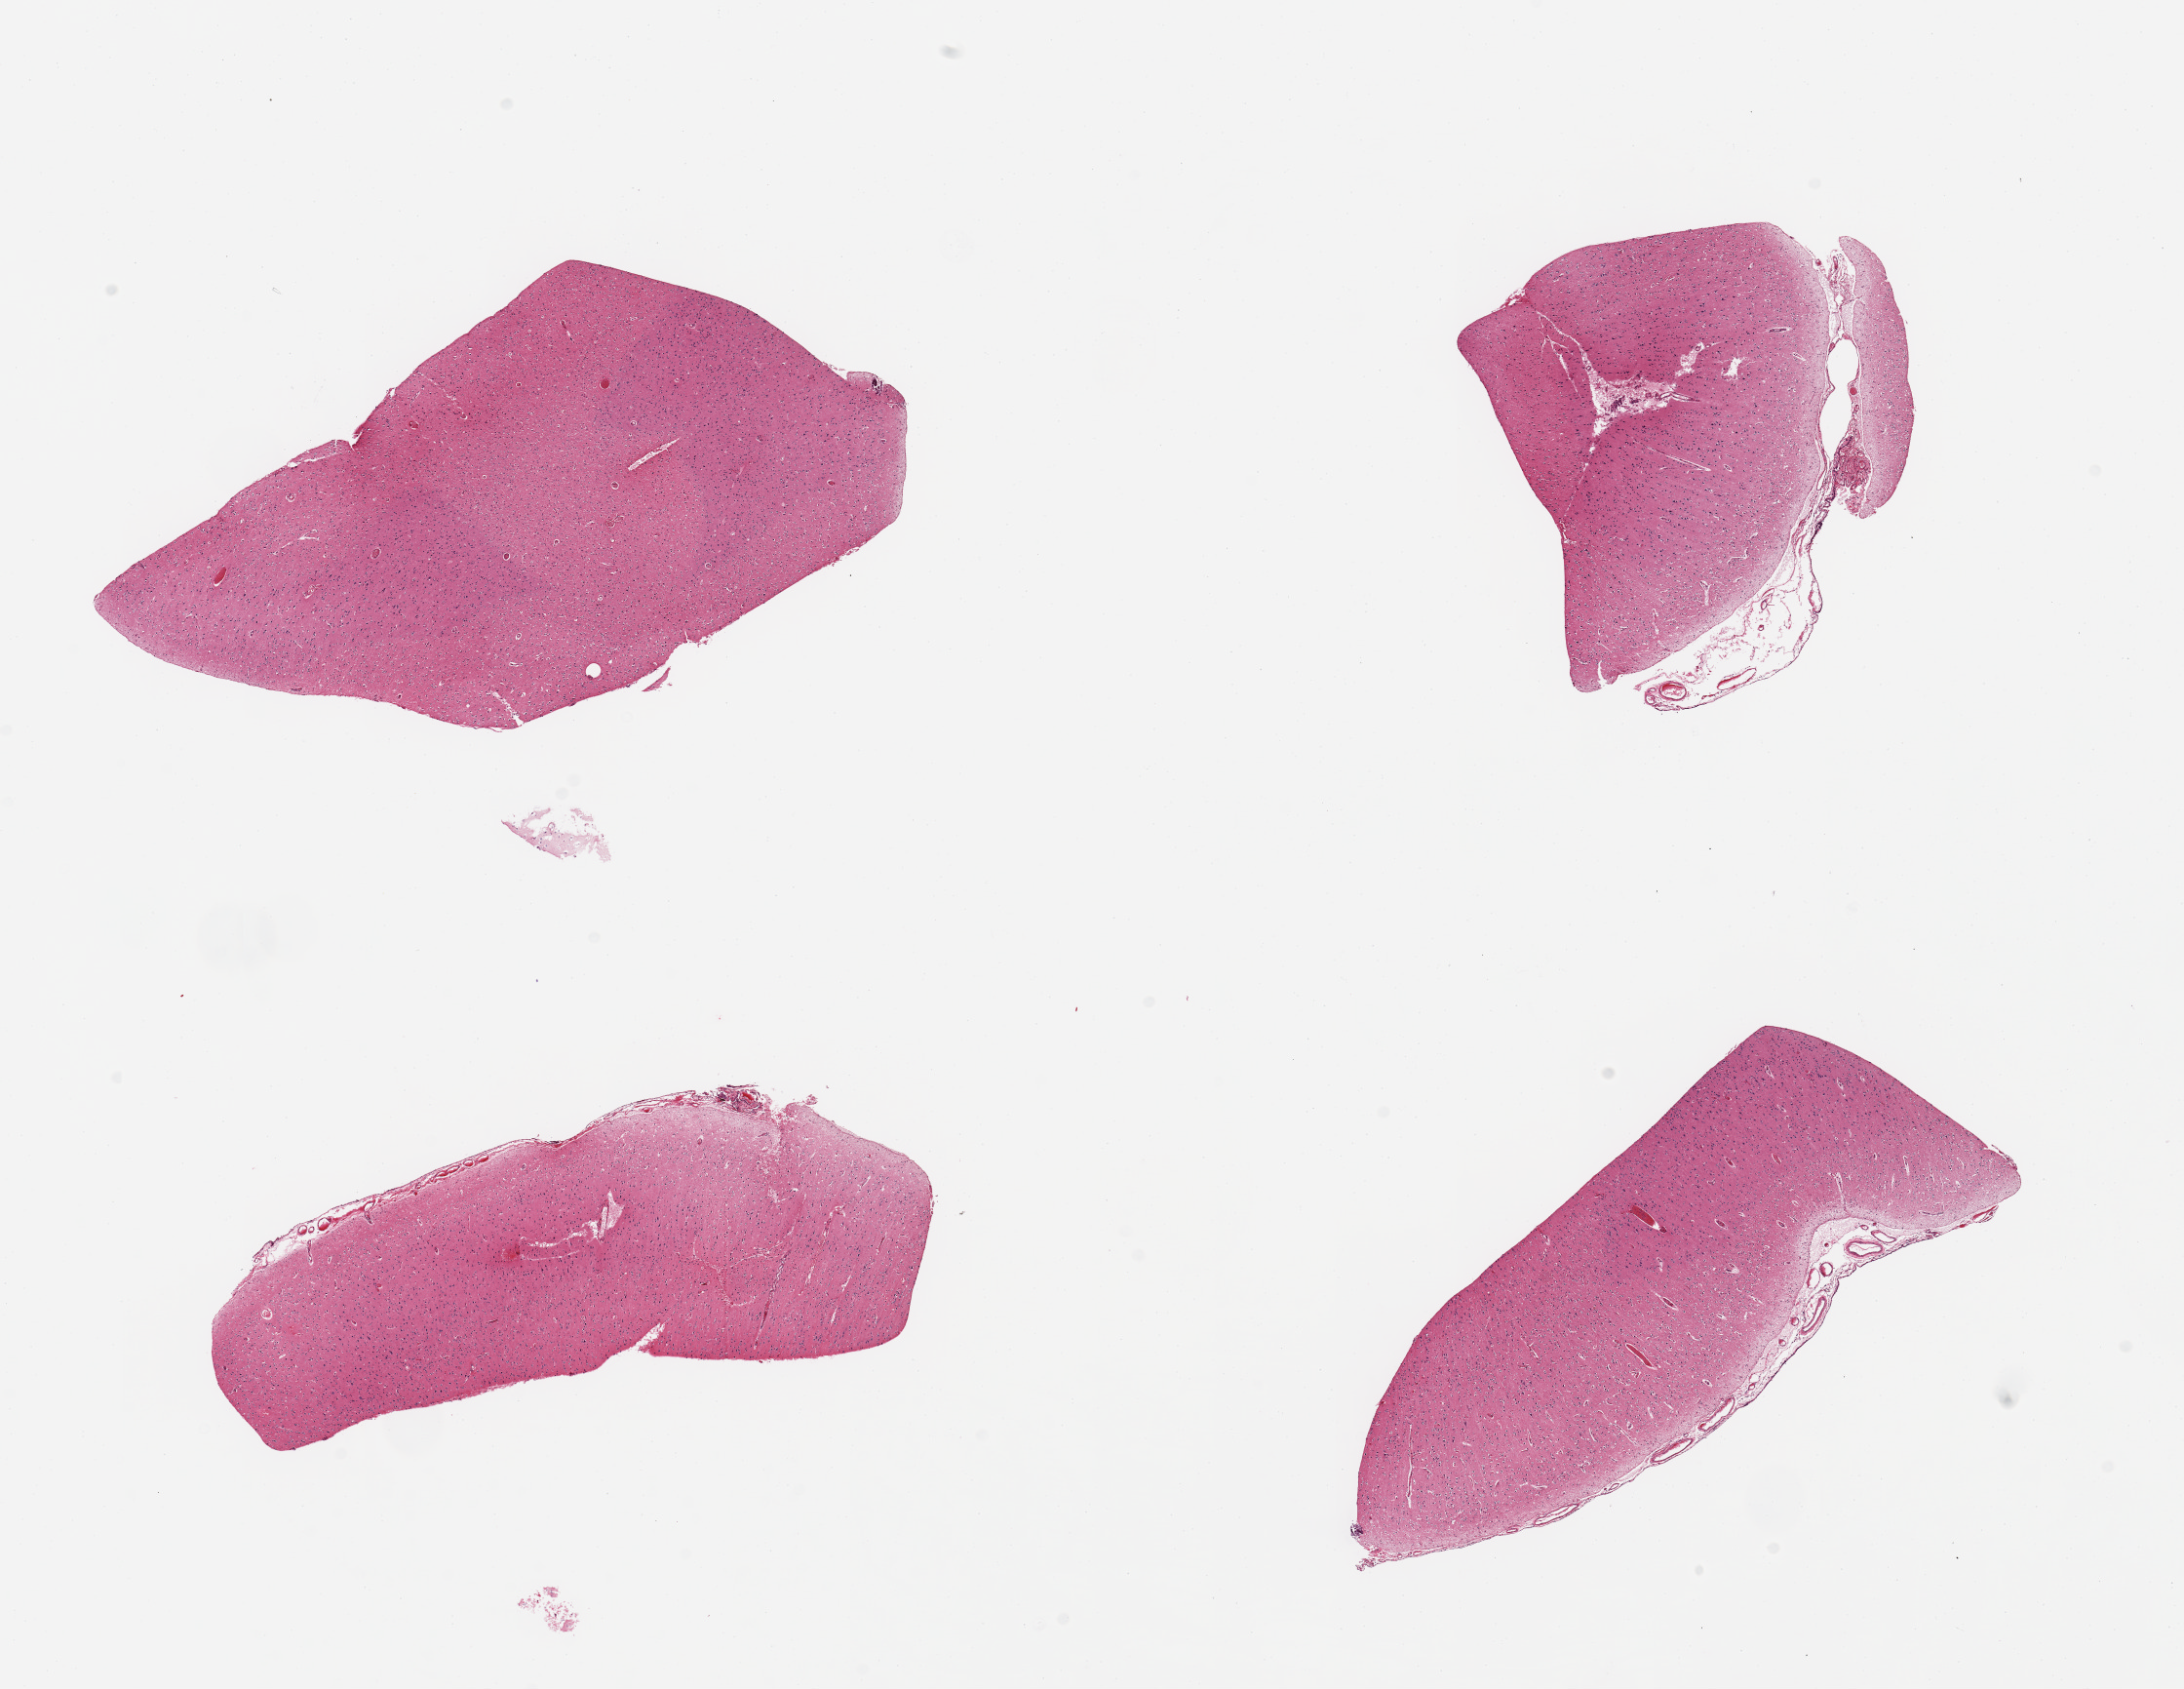
Digitized hematoxylin and eosin (H&E)-stained section, brightfield, a low-resolution overview of the entire scanned area, about 17.7 x 13.7 mm (acquisition: 20x scan). PAXgene-fixed, paraffin-embedded tissue. Section of cerebral cortex (target tissue). Donor tissue sample. Donor sex: female.
Review note (as recorded): 4 pieces.